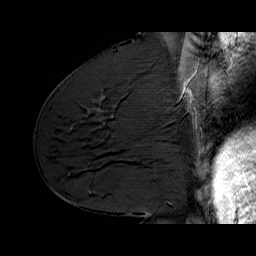
Breast MRI (dynamic contrast-enhanced), one sagittal slice; dynamic contrast-enhanced series, time point 2 of 6 at this slice position (early post-contrast); 1.5 T; TE 6.4 ms, TR 32.9 ms; 4 mm slice thickness; 256 × 256 image matrix. Female patient. From the clinical record (not read from this slice): setting: breast cancer imaged before/during neoadjuvant chemotherapy; receptor status: HER2-positive.
Structures marked on this image (semi-automatic segmentation, software-assisted and operator-edited):
- analysis volume of interest (the breast-tissue region the enhancement analysis was run in; not a lesion): box from (x=138, y=62) to (x=210, y=128) px
- tumour enhancement mask (voxels above the 100 % enhancement threshold inside the analysis volume of interest): (x=182, y=76)–(x=193, y=103)